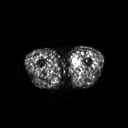
FDG PET of an extremity soft-tissue mass (from a PET/CT study), one axial slice; slice 232 of 311 in the series (ordered by position); 3.27 mm slice thickness; 128 × 128 image matrix, field of view 500 × 500 mm. Male patient, age 29 years. From the clinical record (not read from this slice): histological type: mixoid liposarcoma; grade: low; site of the primary tumour: left thigh.
Structures marked on this image (expert contour drawn on MRI and transferred to this co-registered scan by the dataset authors):
- gross tumour volume (mass): bounding box <71,56,82,69> (left, top, right, bottom; pixels)